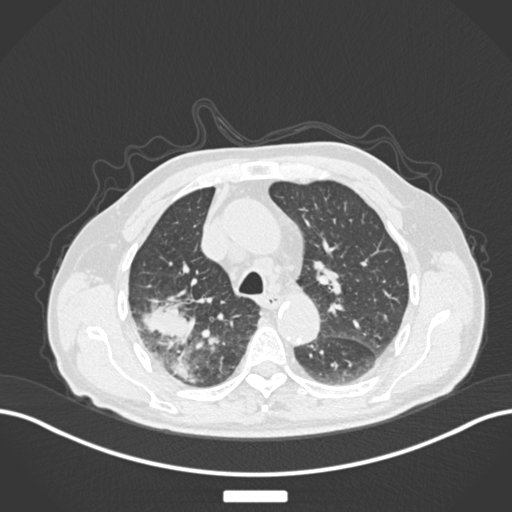
Chest CT, one axial slice; position 131 of 201 along the scan axis; reconstruction kernel B30f; 120 kVp; lung window (W 1500 / L -600 HU); 1 mm slice thickness; 512 × 512 image matrix, field of view 400 × 400 mm. Male patient, age 72 years. From the clinical record (not read from this slice): clinical TNM (as recorded): T3 N2 M0.
Outlined on this slice (rectangle marked by the reading radiologist):
- lung tumour (recorded histology: adenocarcinoma): bounding box (x1, y1, x2, y2) in pixels: (143, 300, 195, 345)